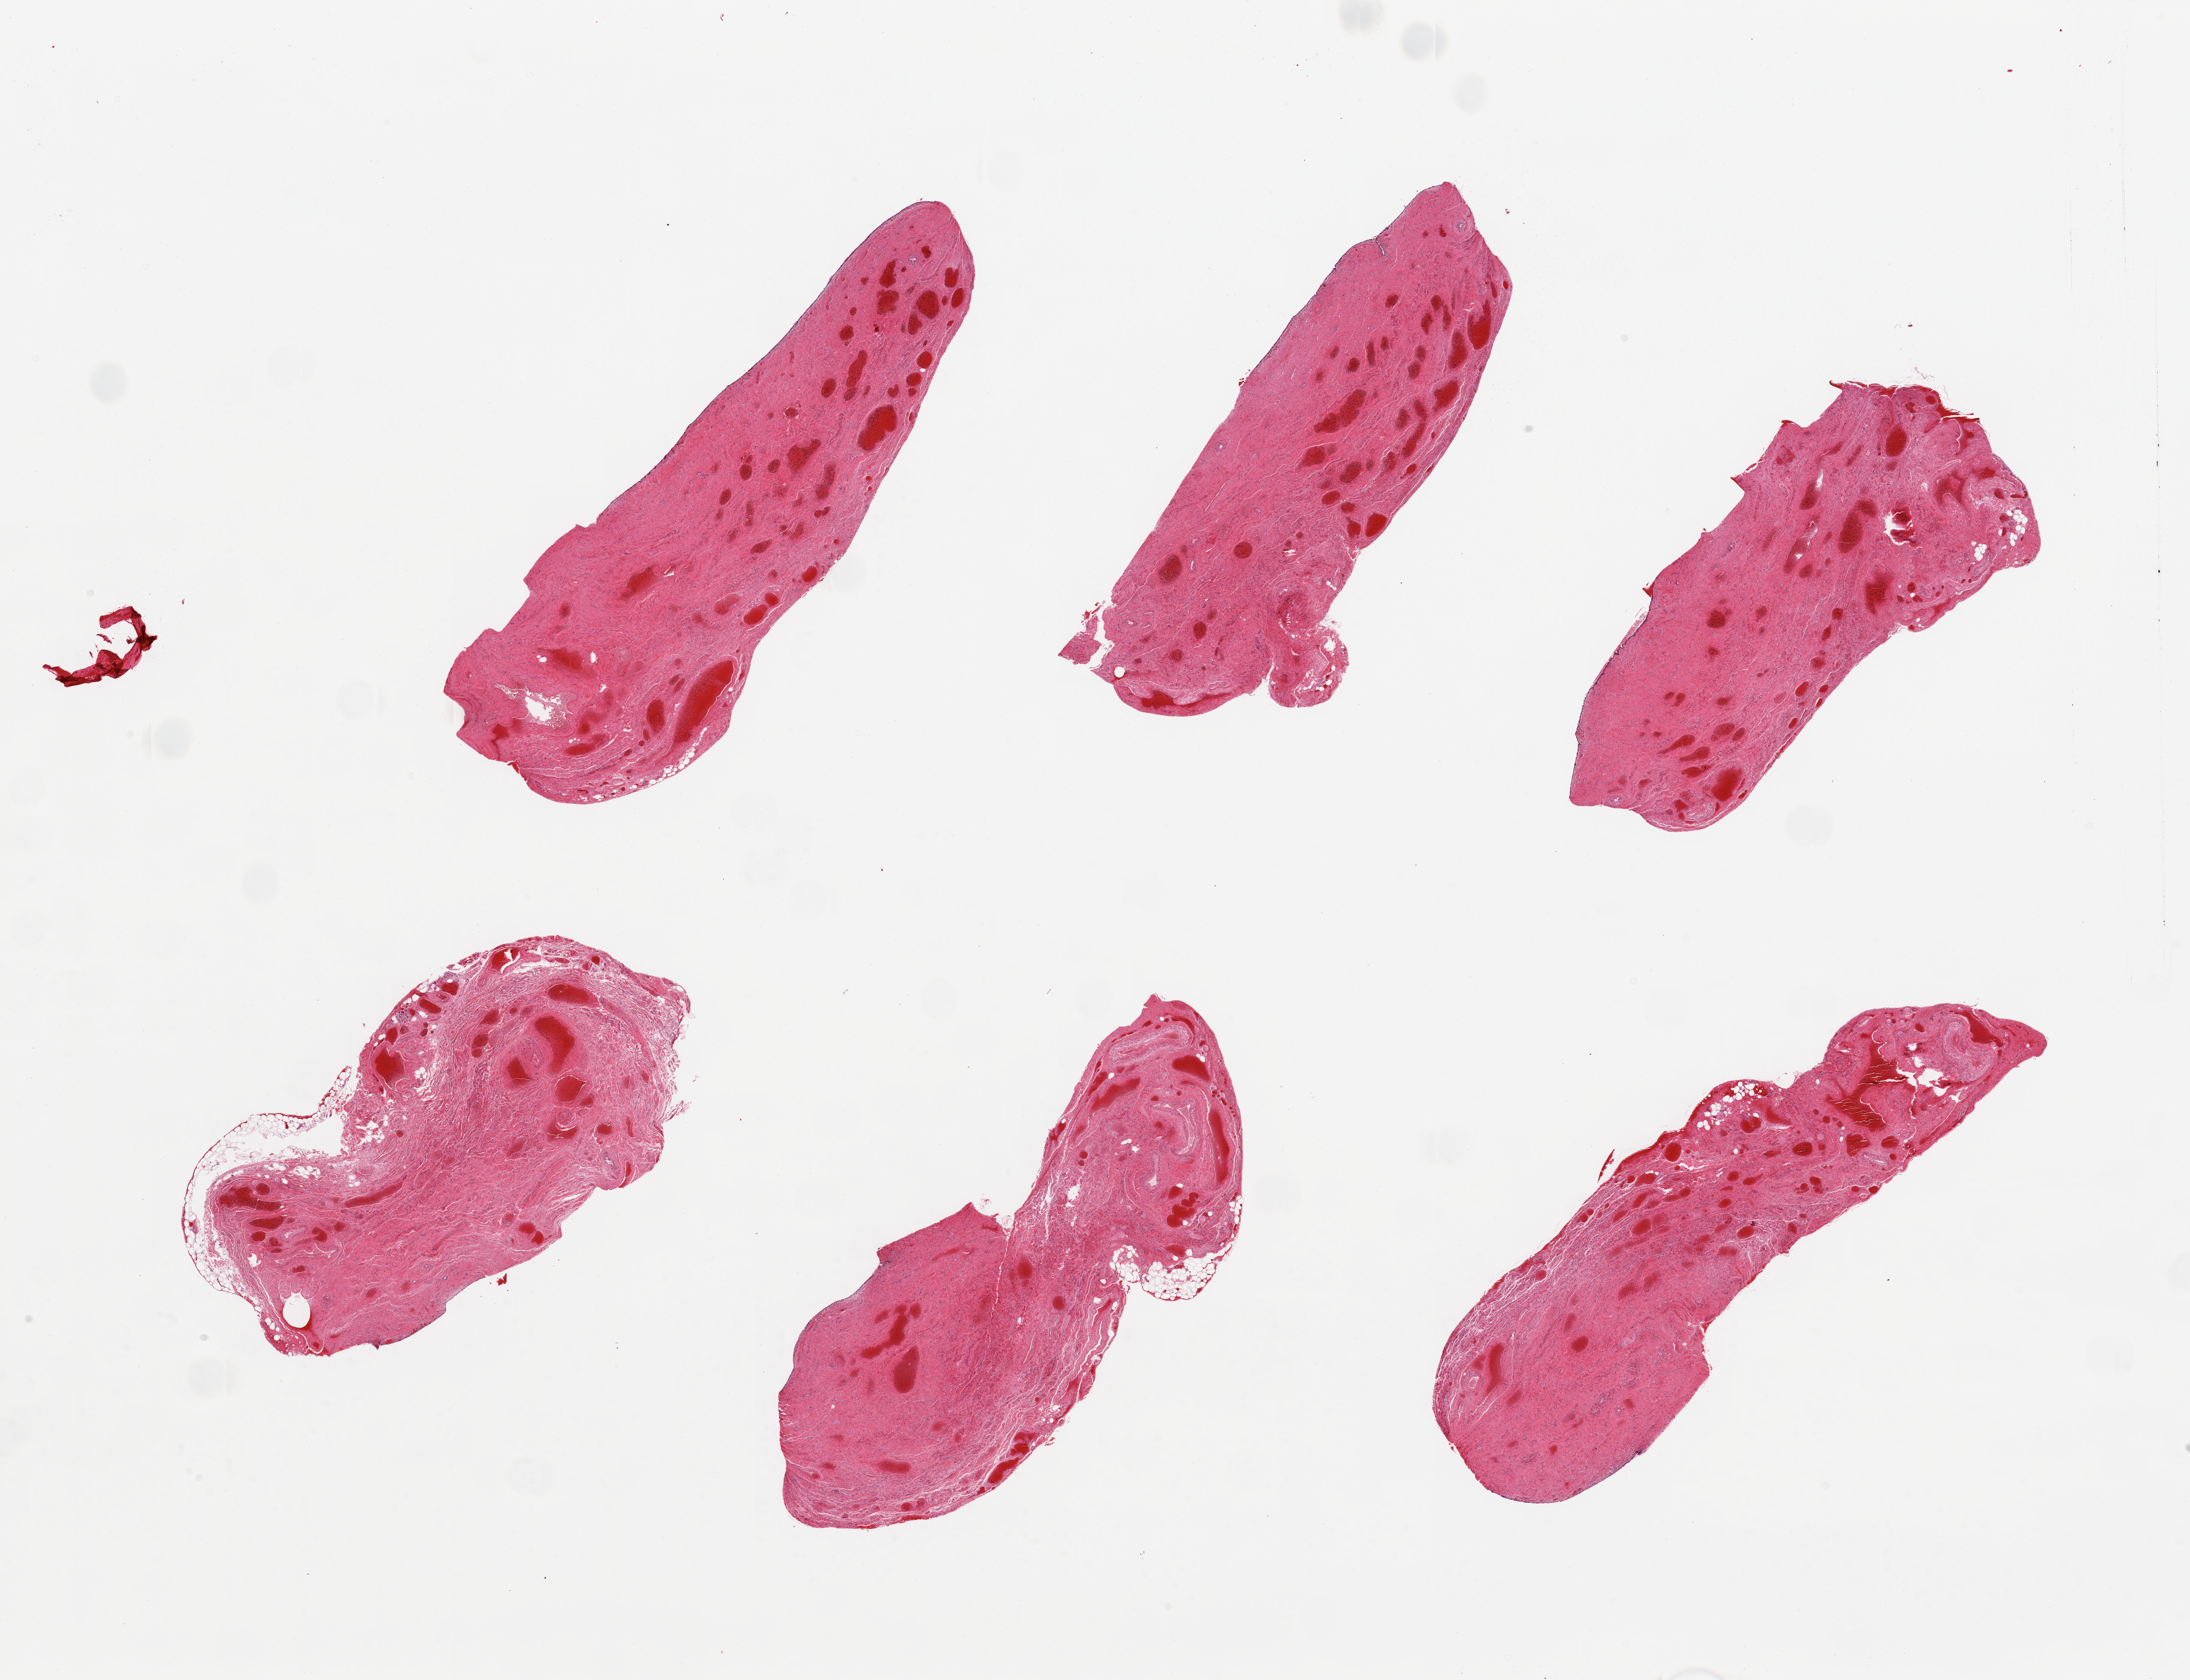
H&E whole-slide image — whole scanned area (about 28.5 x 21.9 mm) shown as a low-resolution overview; PAXgene-fixed, paraffin-embedded tissue; section of vagina (target tissue); donor tissue sample.
Review note (as recorded): 6 pieces; no epithelium; only congested wall.